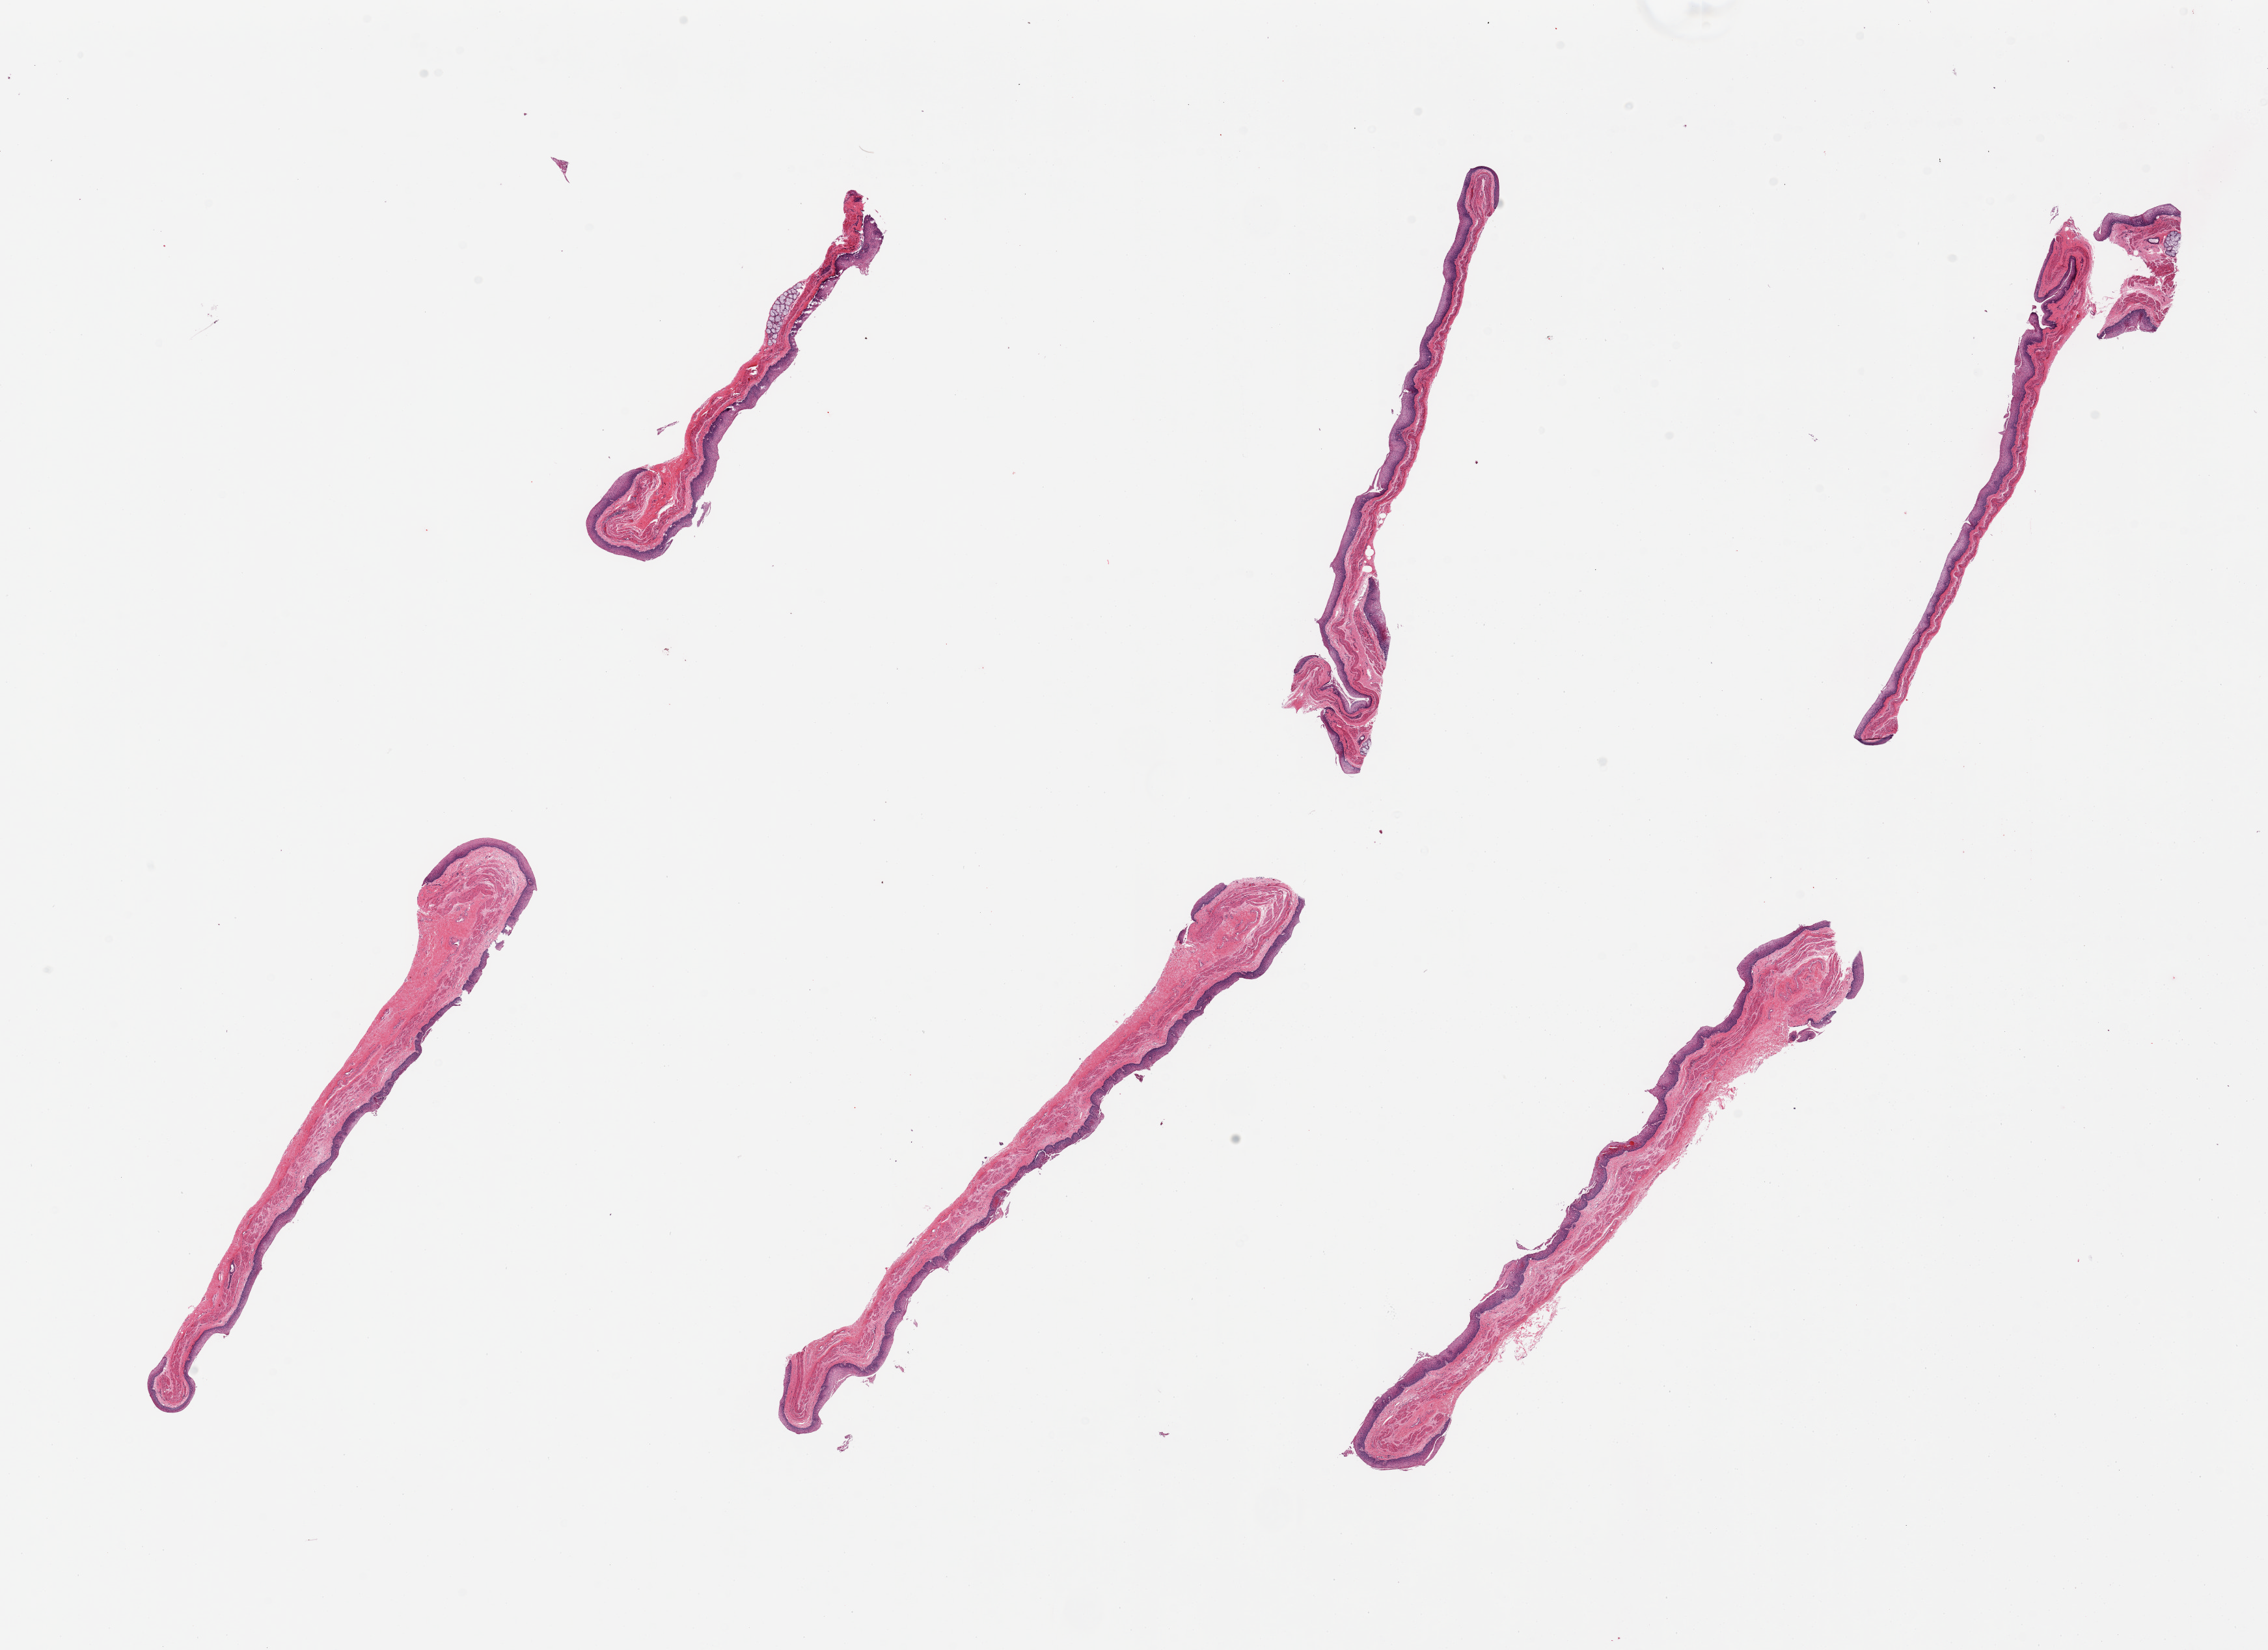
Hematoxylin and eosin (H&E) whole-slide image, brightfield — whole scanned area (about 27.6 x 20.1 mm, slide scanned at 20x) shown as a low-resolution overview, PAXgene-fixed paraffin-embedded (PFPE) section, section of esophageal mucous membrane (target tissue), donor tissue sample. Donor sex: female.
• pathologist's review note for this sample: 6 pieces